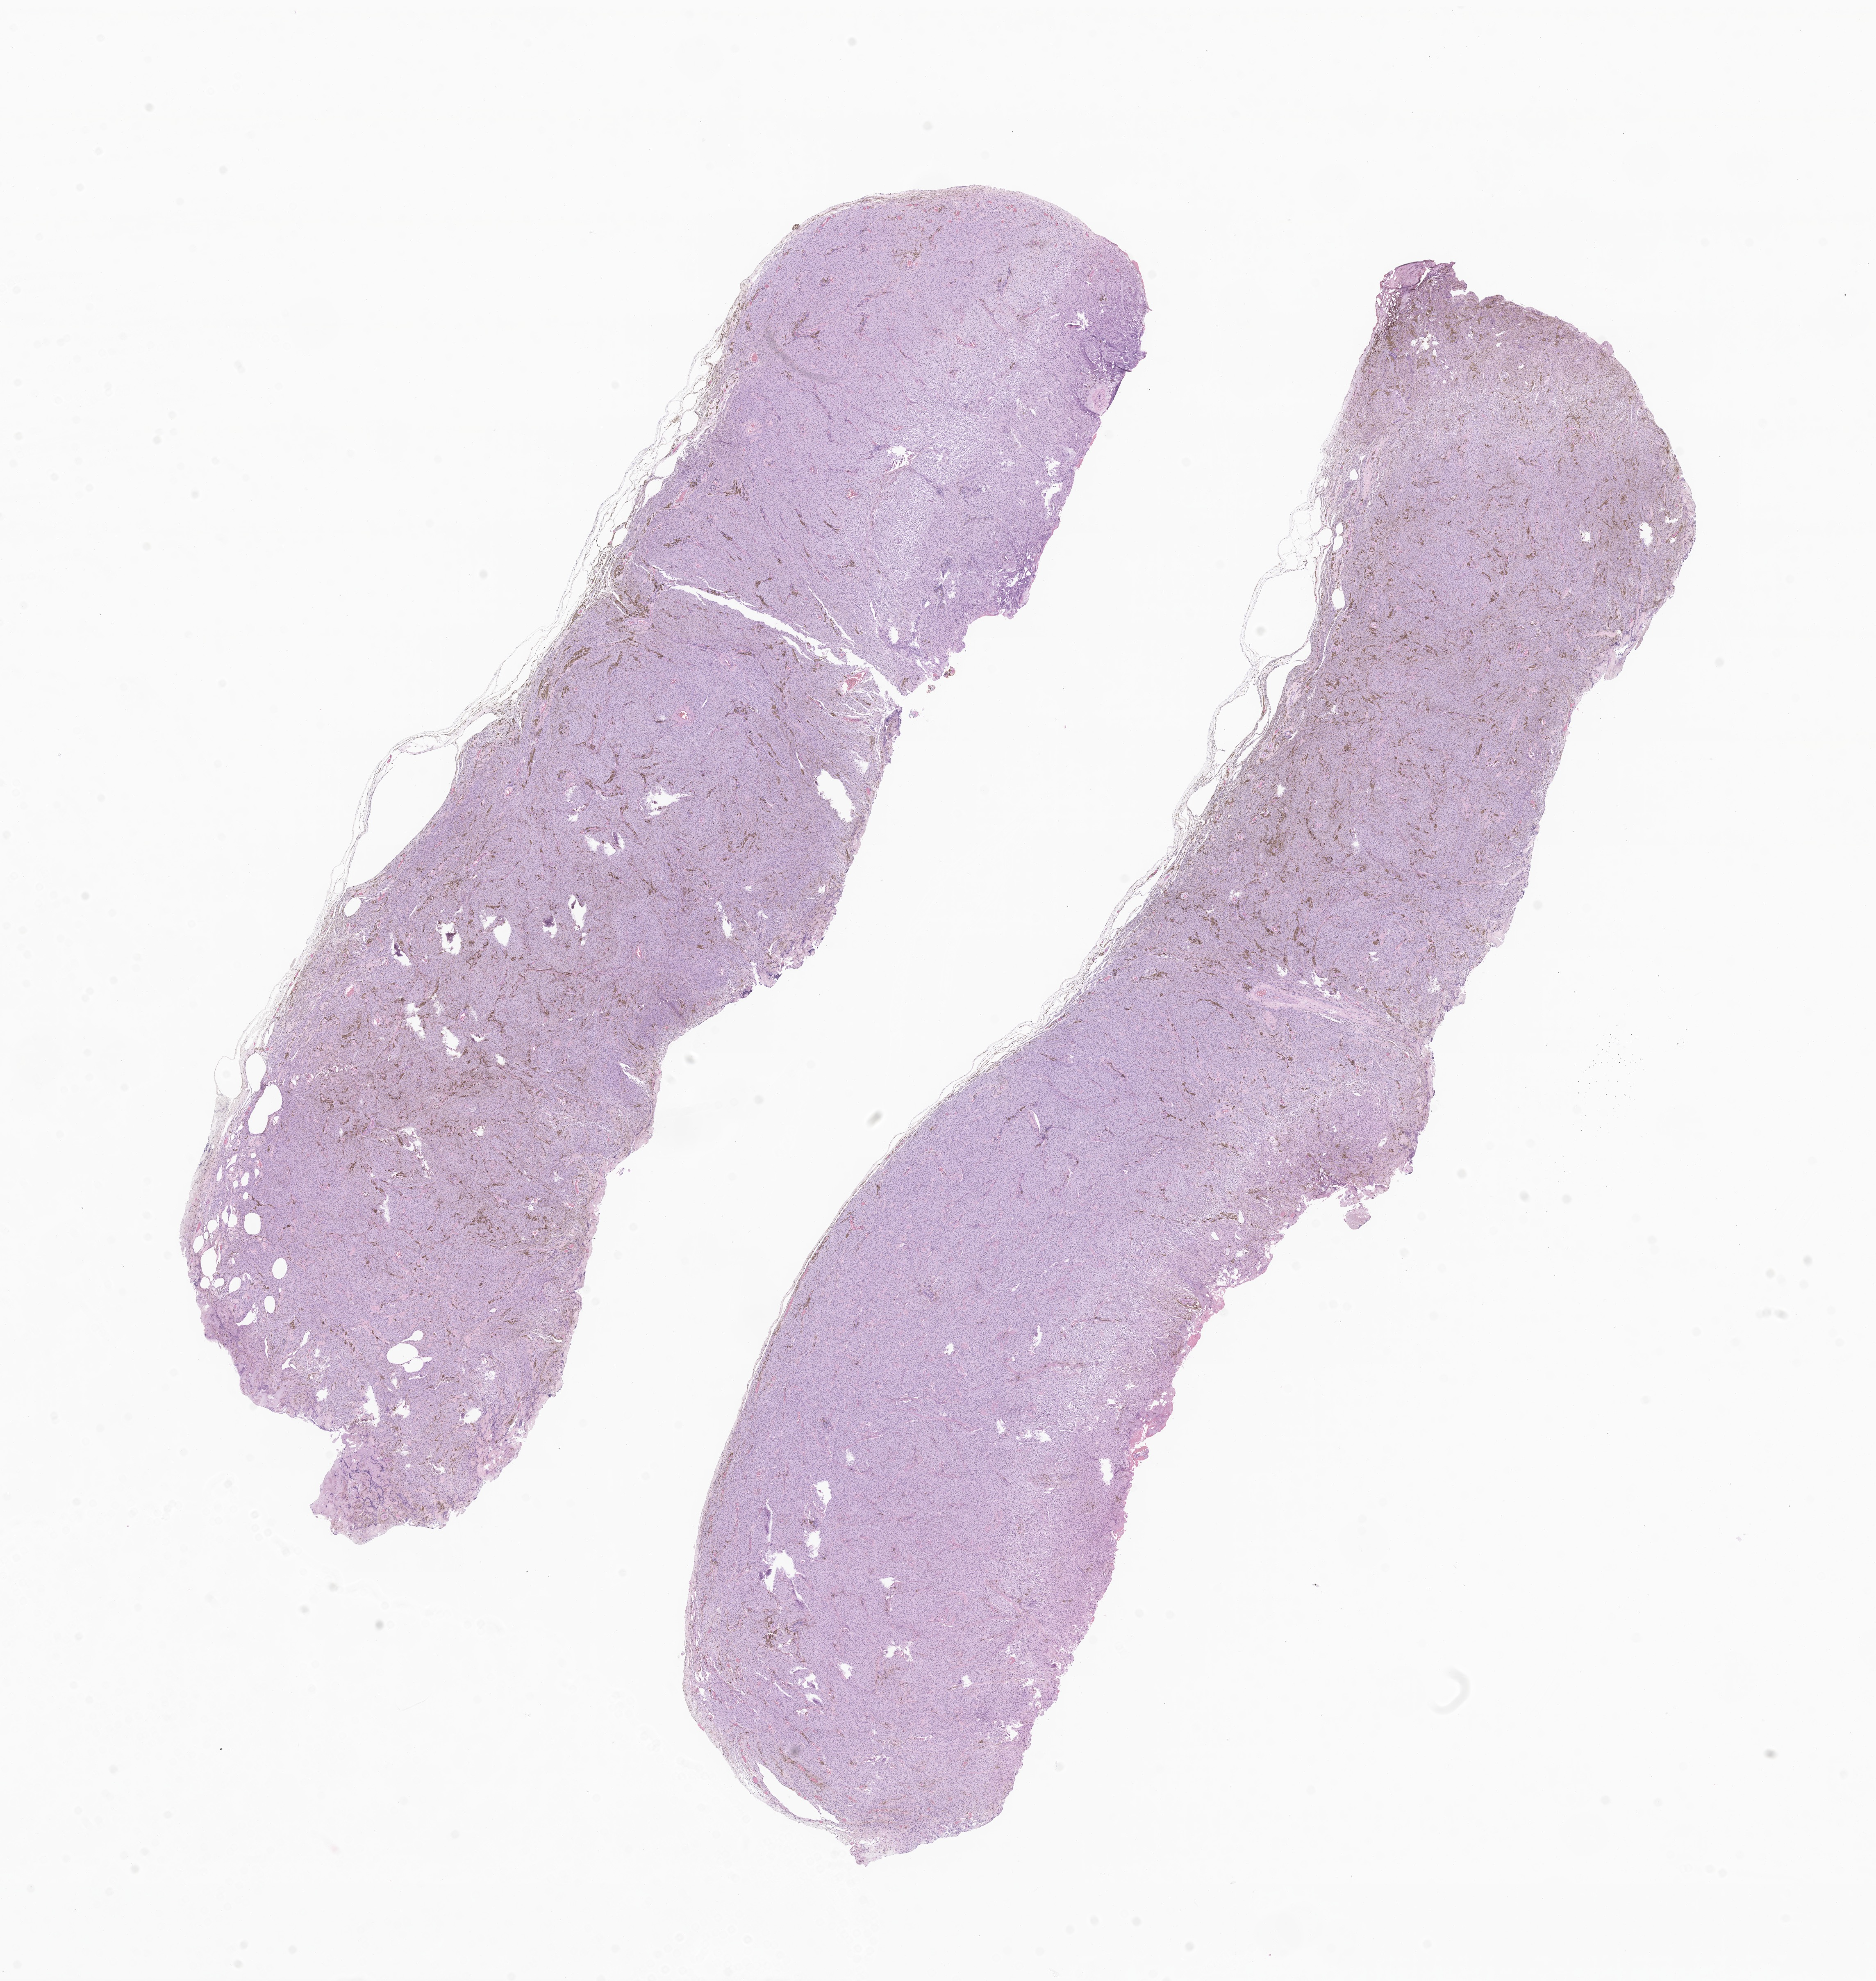
Whole-slide image, haematoxylin and eosin stain of tumor tissue from the spinal cord — low-resolution overview of the scanned area, about 19.3 x 20.4 mm, FFPE section. Patient female; age 200 months (16 years 8 months).
• diagnosis: Meningeal melanocytoma